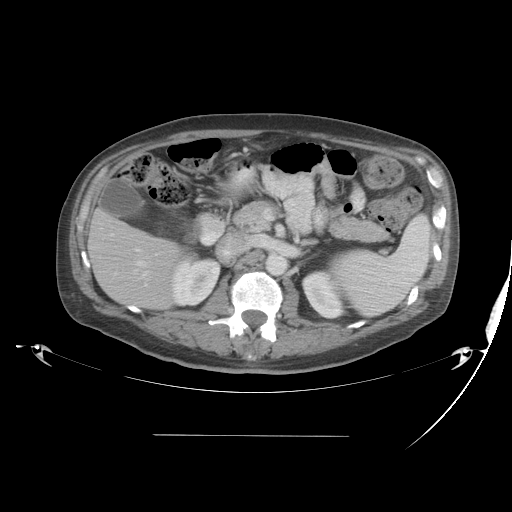
Contrast-enhanced abdominal CT, one axial slice. Slice 20 of 48 in the series (ordered by position). Reconstruction kernel STANDARD. 120 kVp. Intravenous contrast given. Soft-tissue window (W 400 / L 40 HU). 5 mm slice thickness. 512 × 512 image matrix. Male patient, age 65 years. Case-level facts recorded for this patient, not image findings: diagnosis: colorectal cancer liver metastases, imaged before liver resection; multiple liver metastases: yes; largest metastasis: 11 cm; disease in both lobes: yes.
Outlined on this slice (manually delineated by an expert):
- hepatic veins: bounding box [x1, y1, x2, y2] px = [136, 261, 146, 266]
- liver: [90, 211, 182, 309]
- portal vein (with intrahepatic branches): [98, 232, 150, 286]